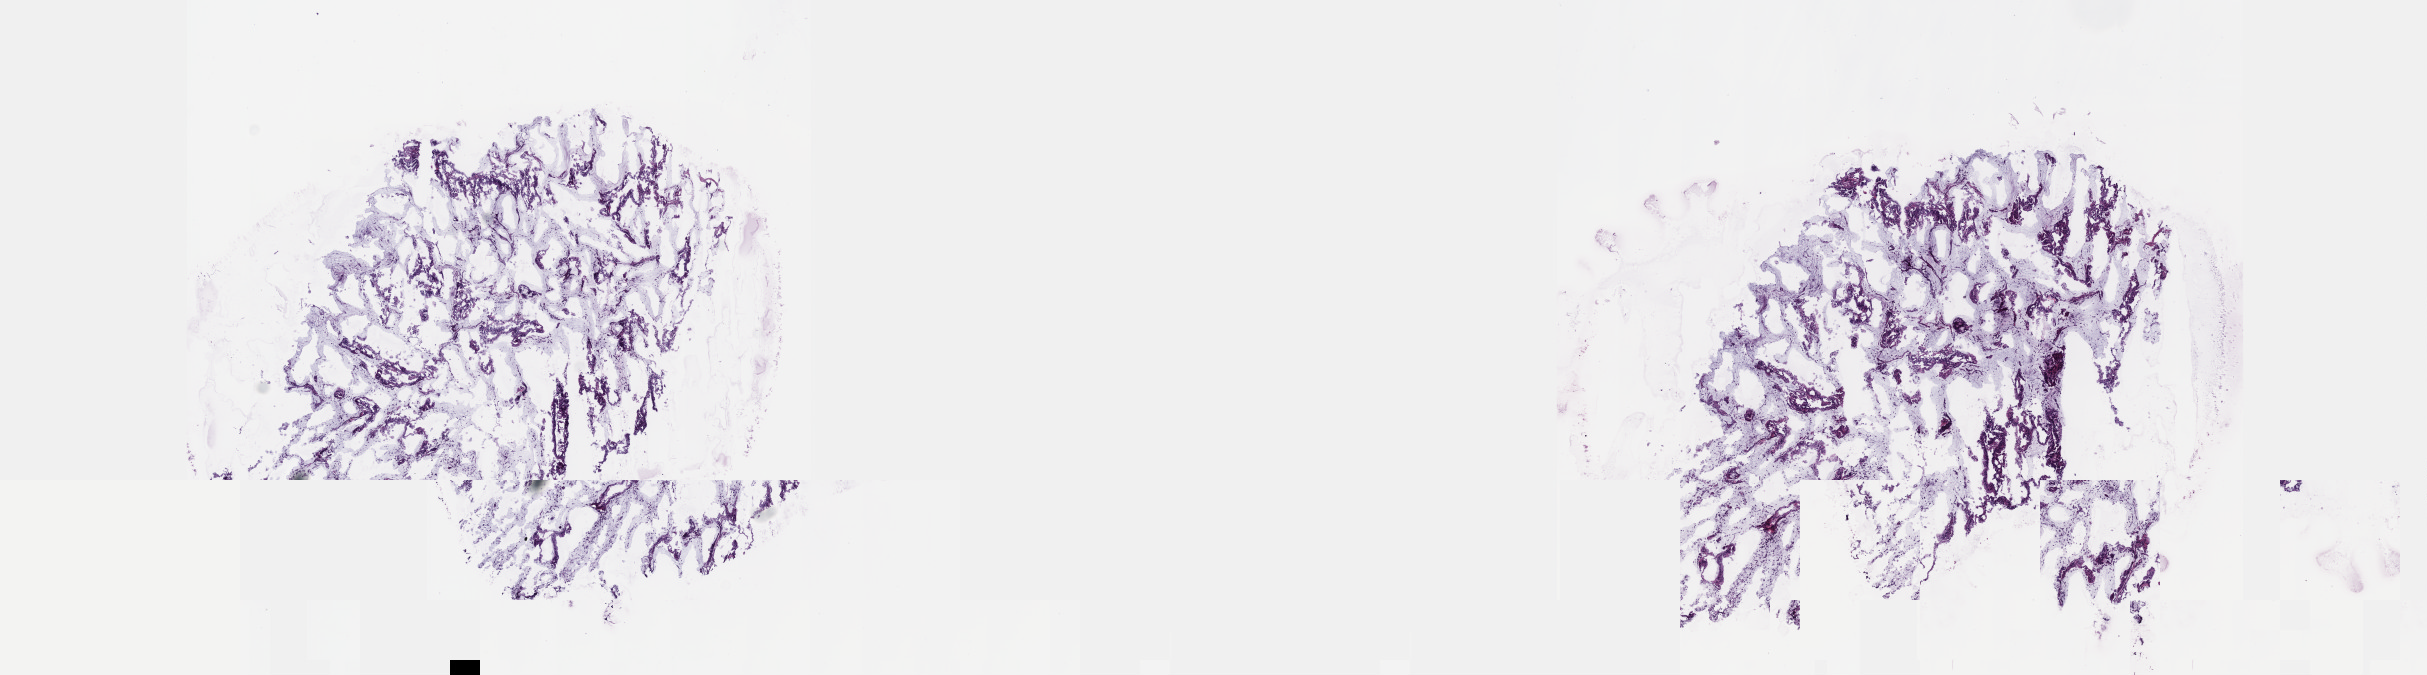
Digitized Hematoxylin and eosin (H&E) stained tissue section (whole slide) — low-resolution overview of the scanned area, about 19.6 x 5.5 mm (from a 40x scan), frozen section from the top of the tissue portion, sample: primary tumour, cervix. Patient: female, age at initial diagnosis 76 years. Histologic grade: G2 (moderately differentiated). Pathologist review of this section (percent, as recorded): tumour cells 90%, tumour nuclei 90%, normal cells 5%, stromal cells 5%, necrosis 0%. Inflammatory infiltration, as recorded: lymphocyte infiltration 4%, monocyte infiltration 1%, neutrophil infiltration 0%.
• FIGO stage: IB1
• histologic diagnosis: Mucinous adenocarcinoma, endocervical type (cervix uteri)